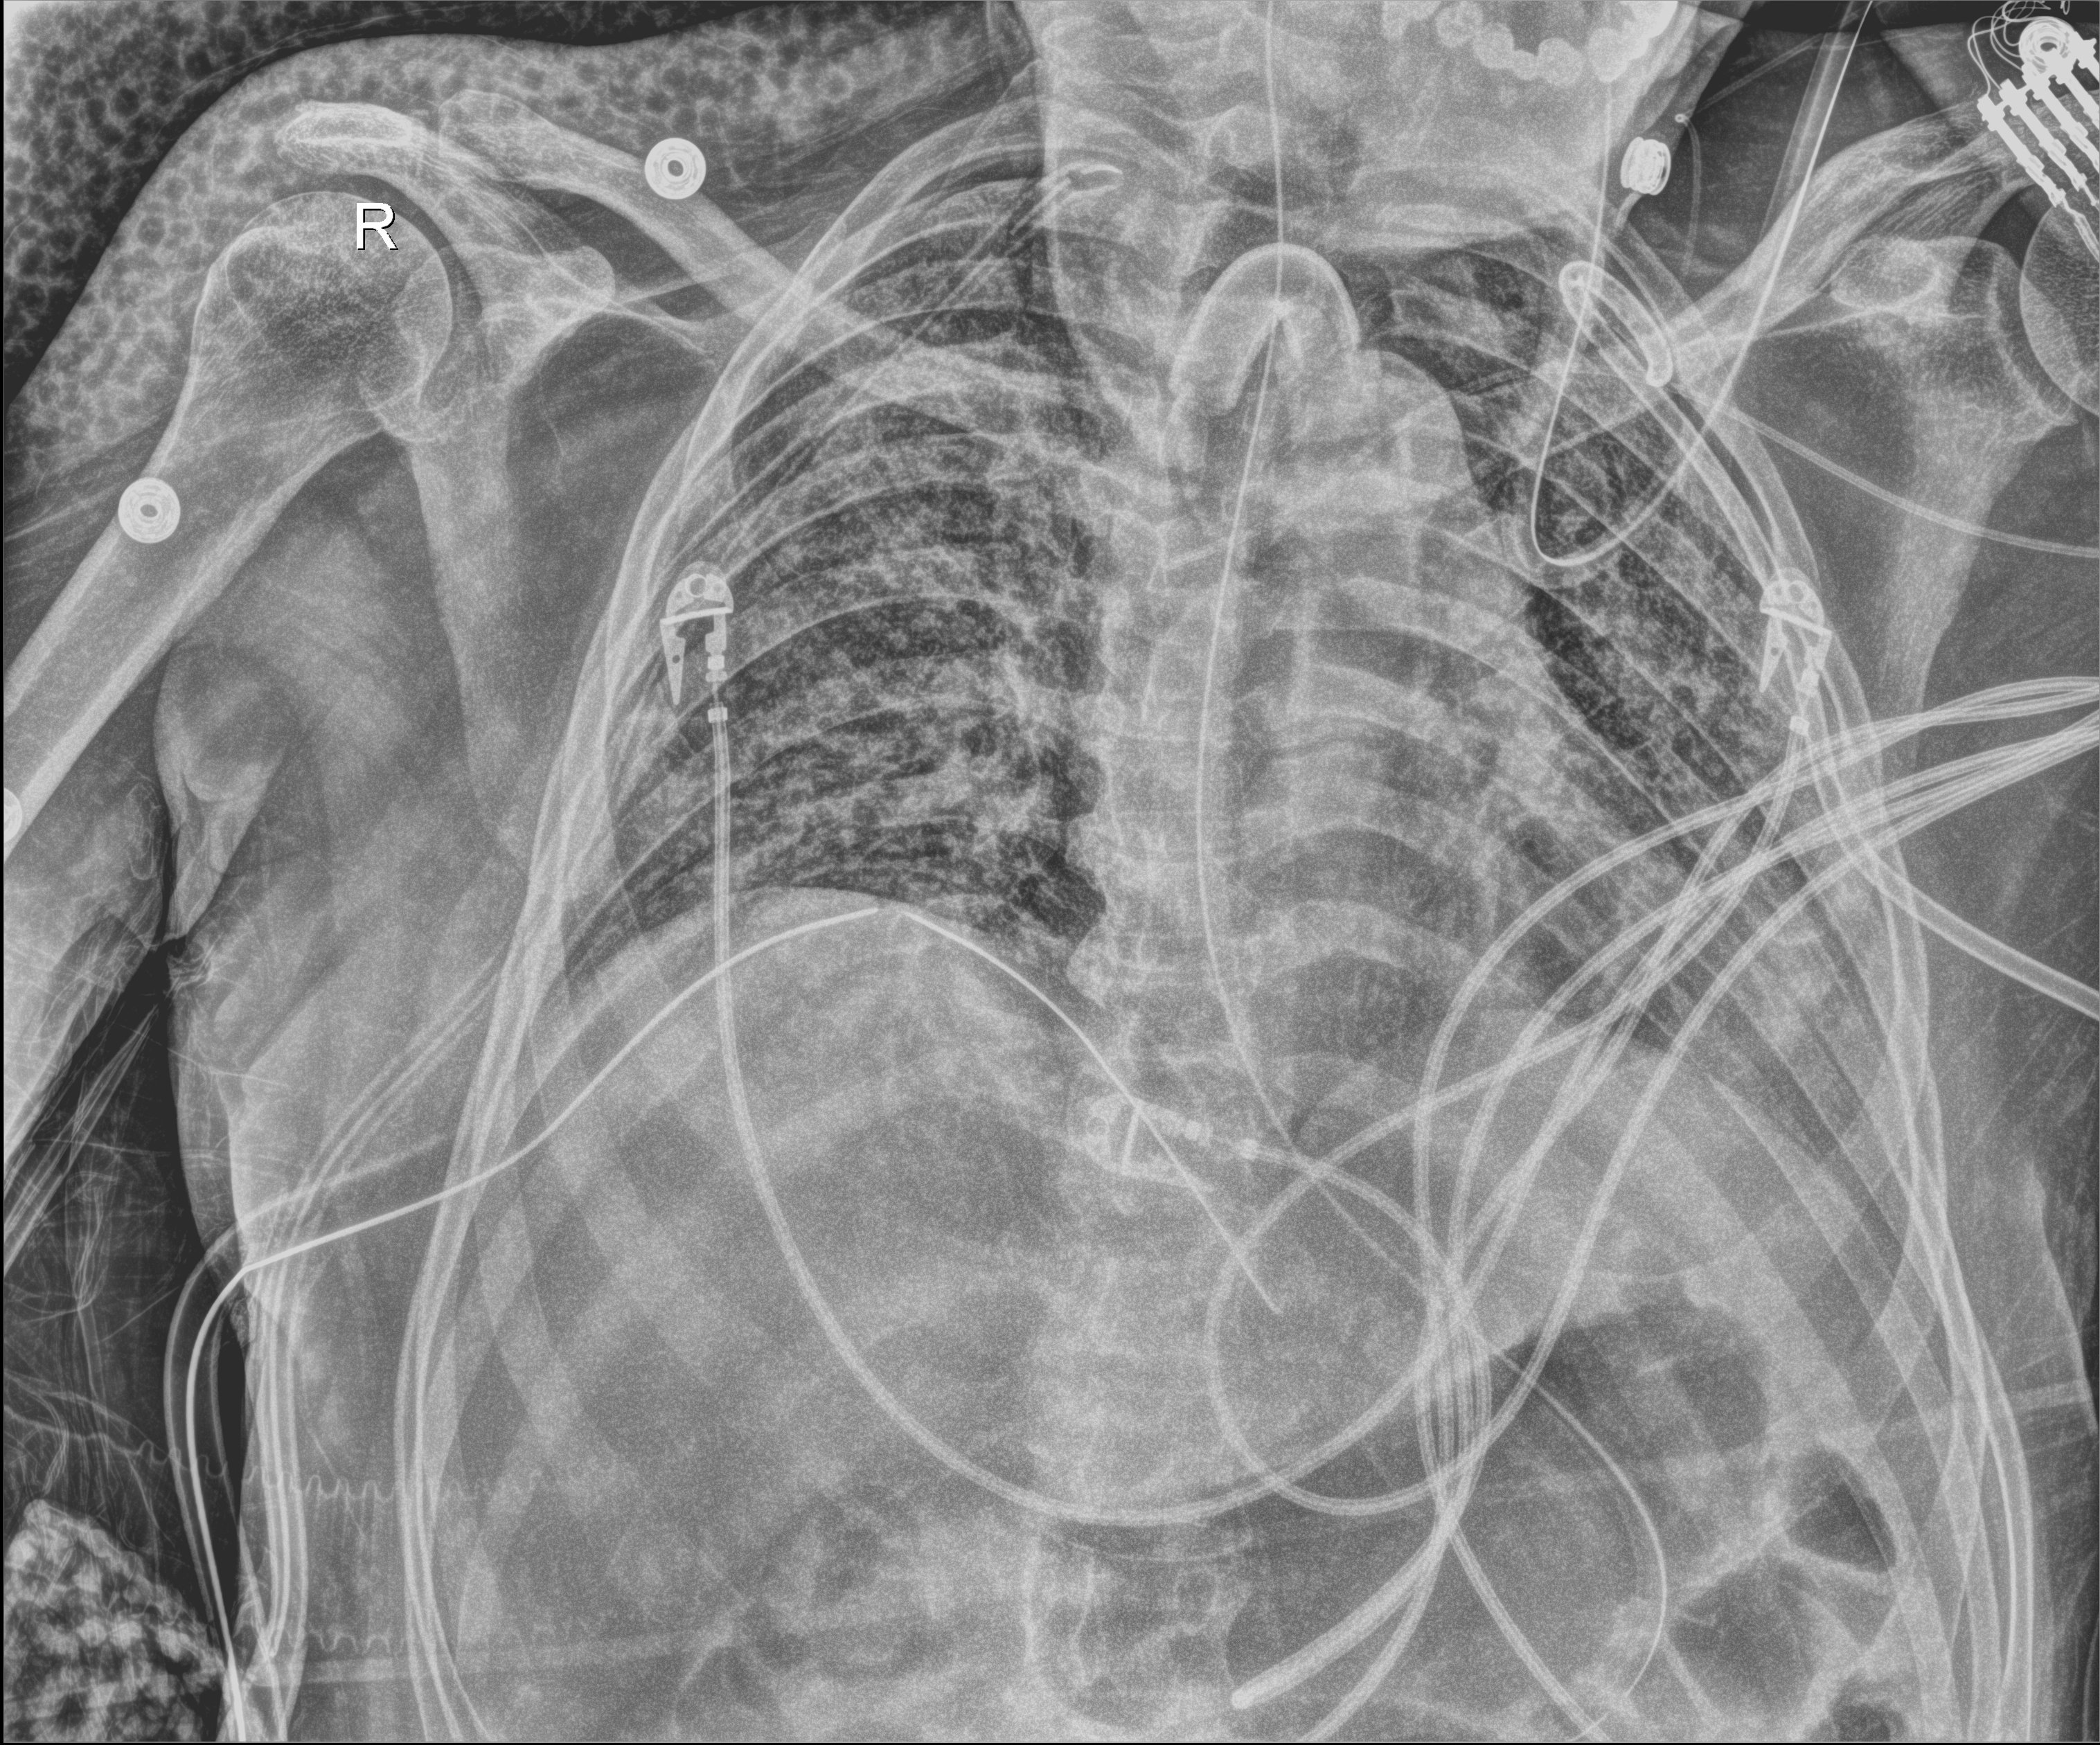
Chest X-ray (portable). Patient hospitalised with COVID-19; male, aged 18–59 years.
Admission-level facts for this patient (not findings on this image; timing relative to this image not recorded):
- other chronic lung disease (admission record): no